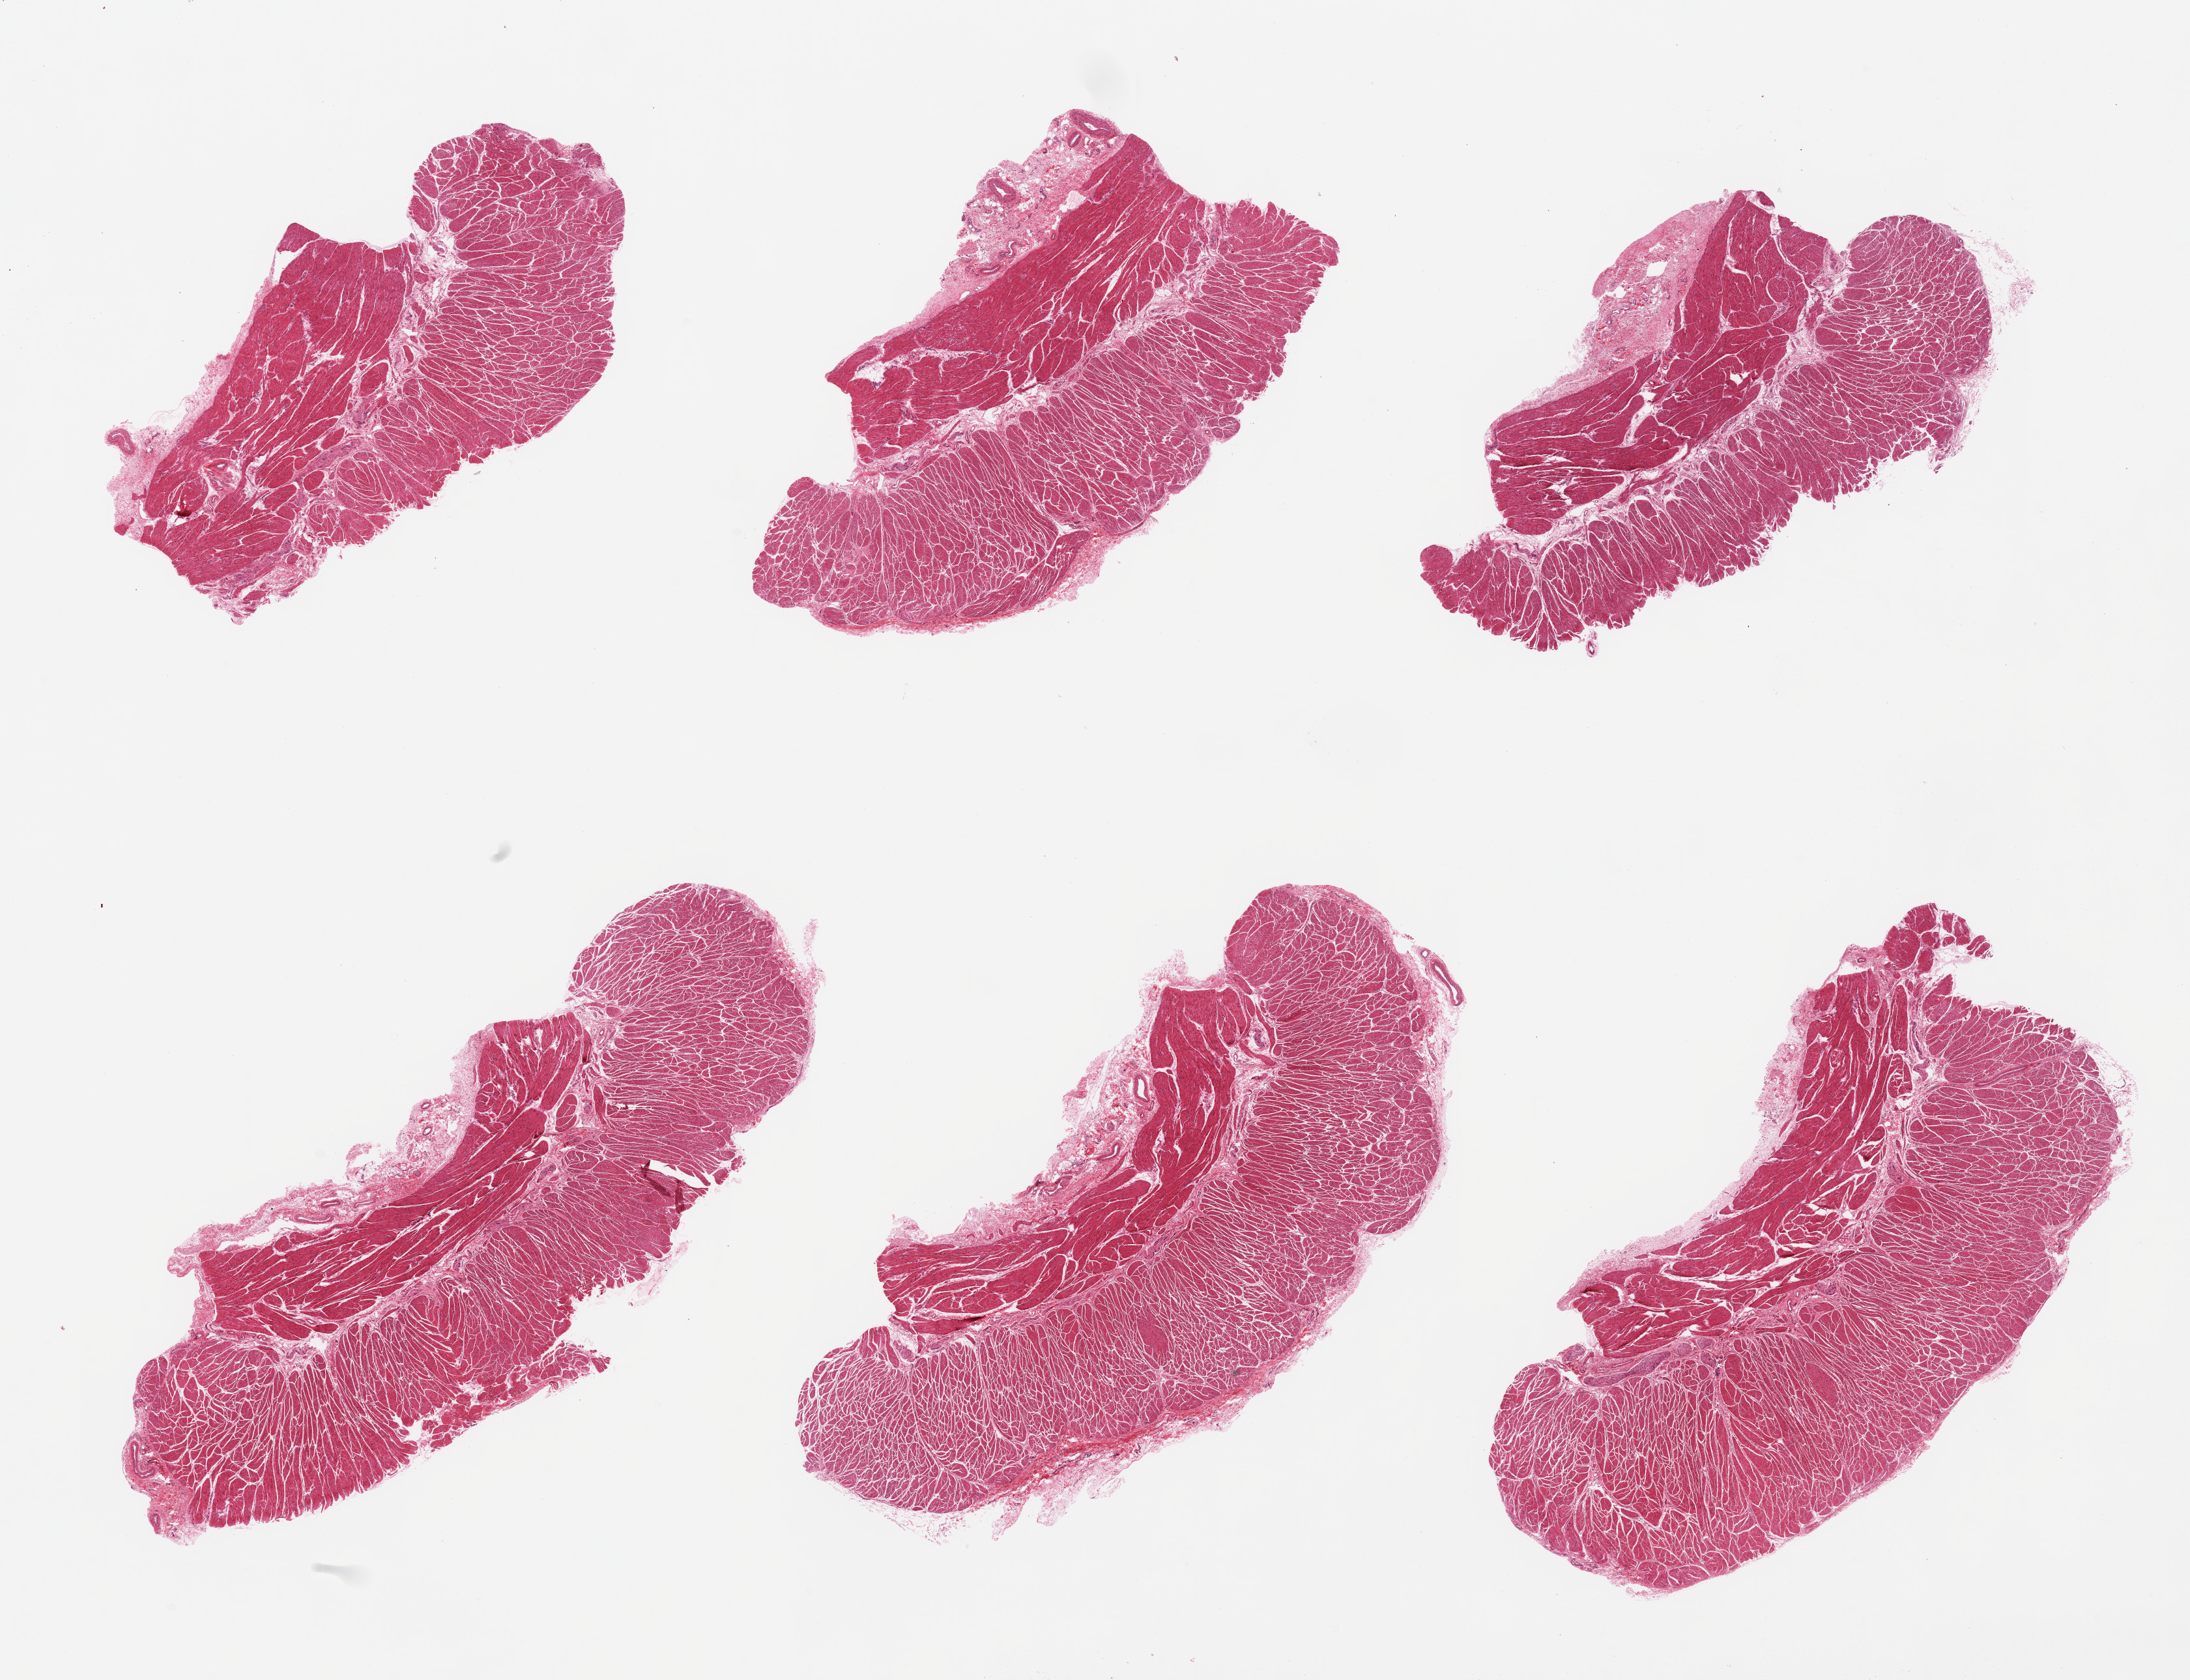
Whole-slide image, H&E stain, shown as a low-resolution overview of the whole scanned area (about 26.6 x 20.4 mm, acquisition: 20x scan), PAXgene-fixed, paraffin-embedded tissue, target tissue: esophageal muscle, donor tissue sample. Donor sex: female.
Reviewer comment on this tissue sample: 6 pieces, all muscularis; trace adherent fat/serosa, good specimens.